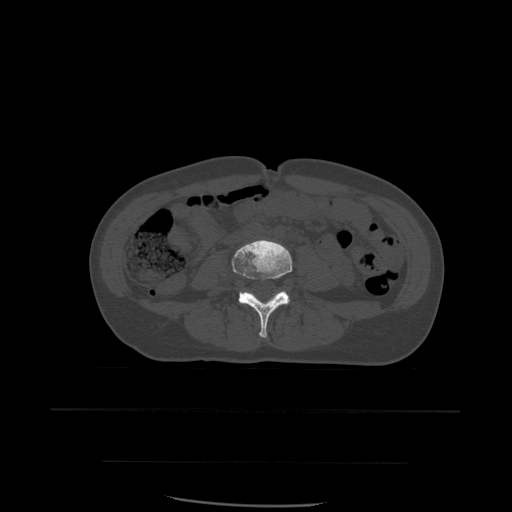
CT including the spine, one axial slice. Slice 169 of 574 in the series (ordered by position). Bone window (W 1800 / L 400 HU). 1.25 mm slice thickness. 512 × 512 image matrix, field of view 392 × 392 mm. Patient age 48 years. Case-level facts recorded for this patient, not image findings: primary cancer: lung.
Annotated regions visible in this slice (semi-automatically segmented with operator editing):
- L4 vertebra: bounding box [x1, y1, x2, y2] px = [232, 240, 293, 338]